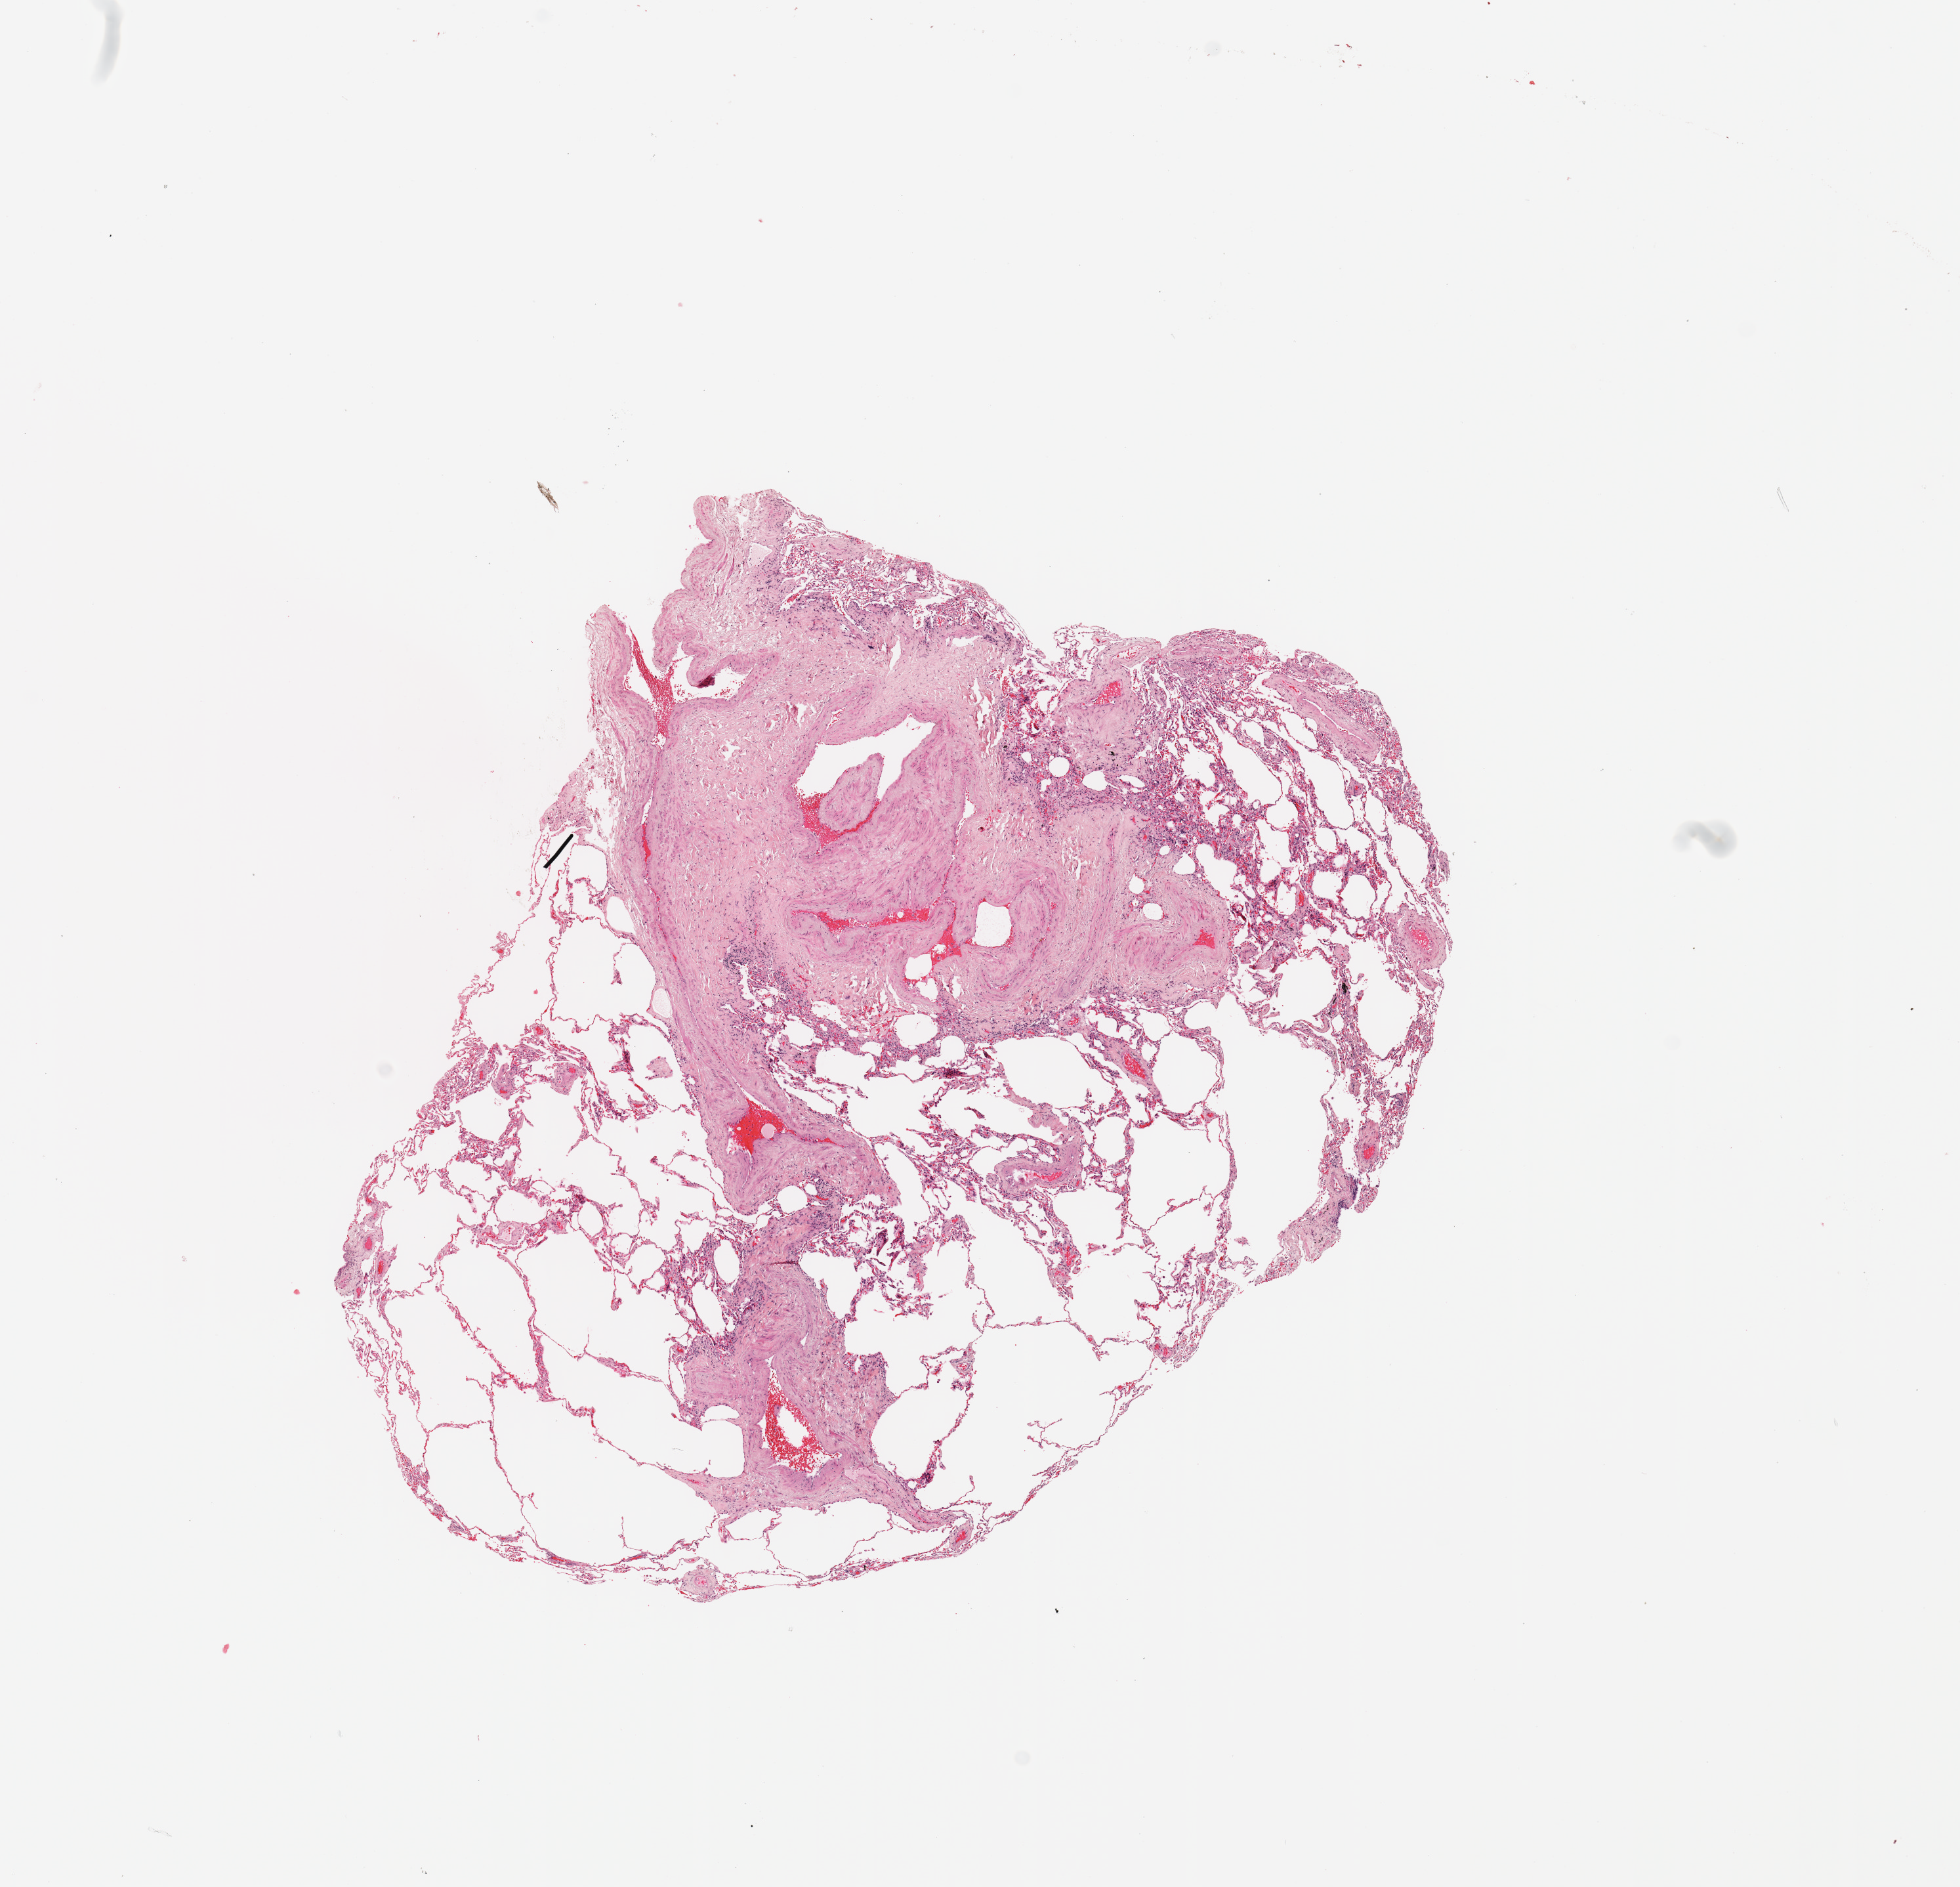
Digitized H&E tissue section (whole slide) — low-resolution overview of the scanned area, about 11.8 x 11.4 mm; normal (non-tumour) tissue sample, sampled site: lung. Male, 78 y/o.
This section: normal (non-tumour) tissue from the same patient. Patient diagnosis: Squamous cell carcinoma, NOS.